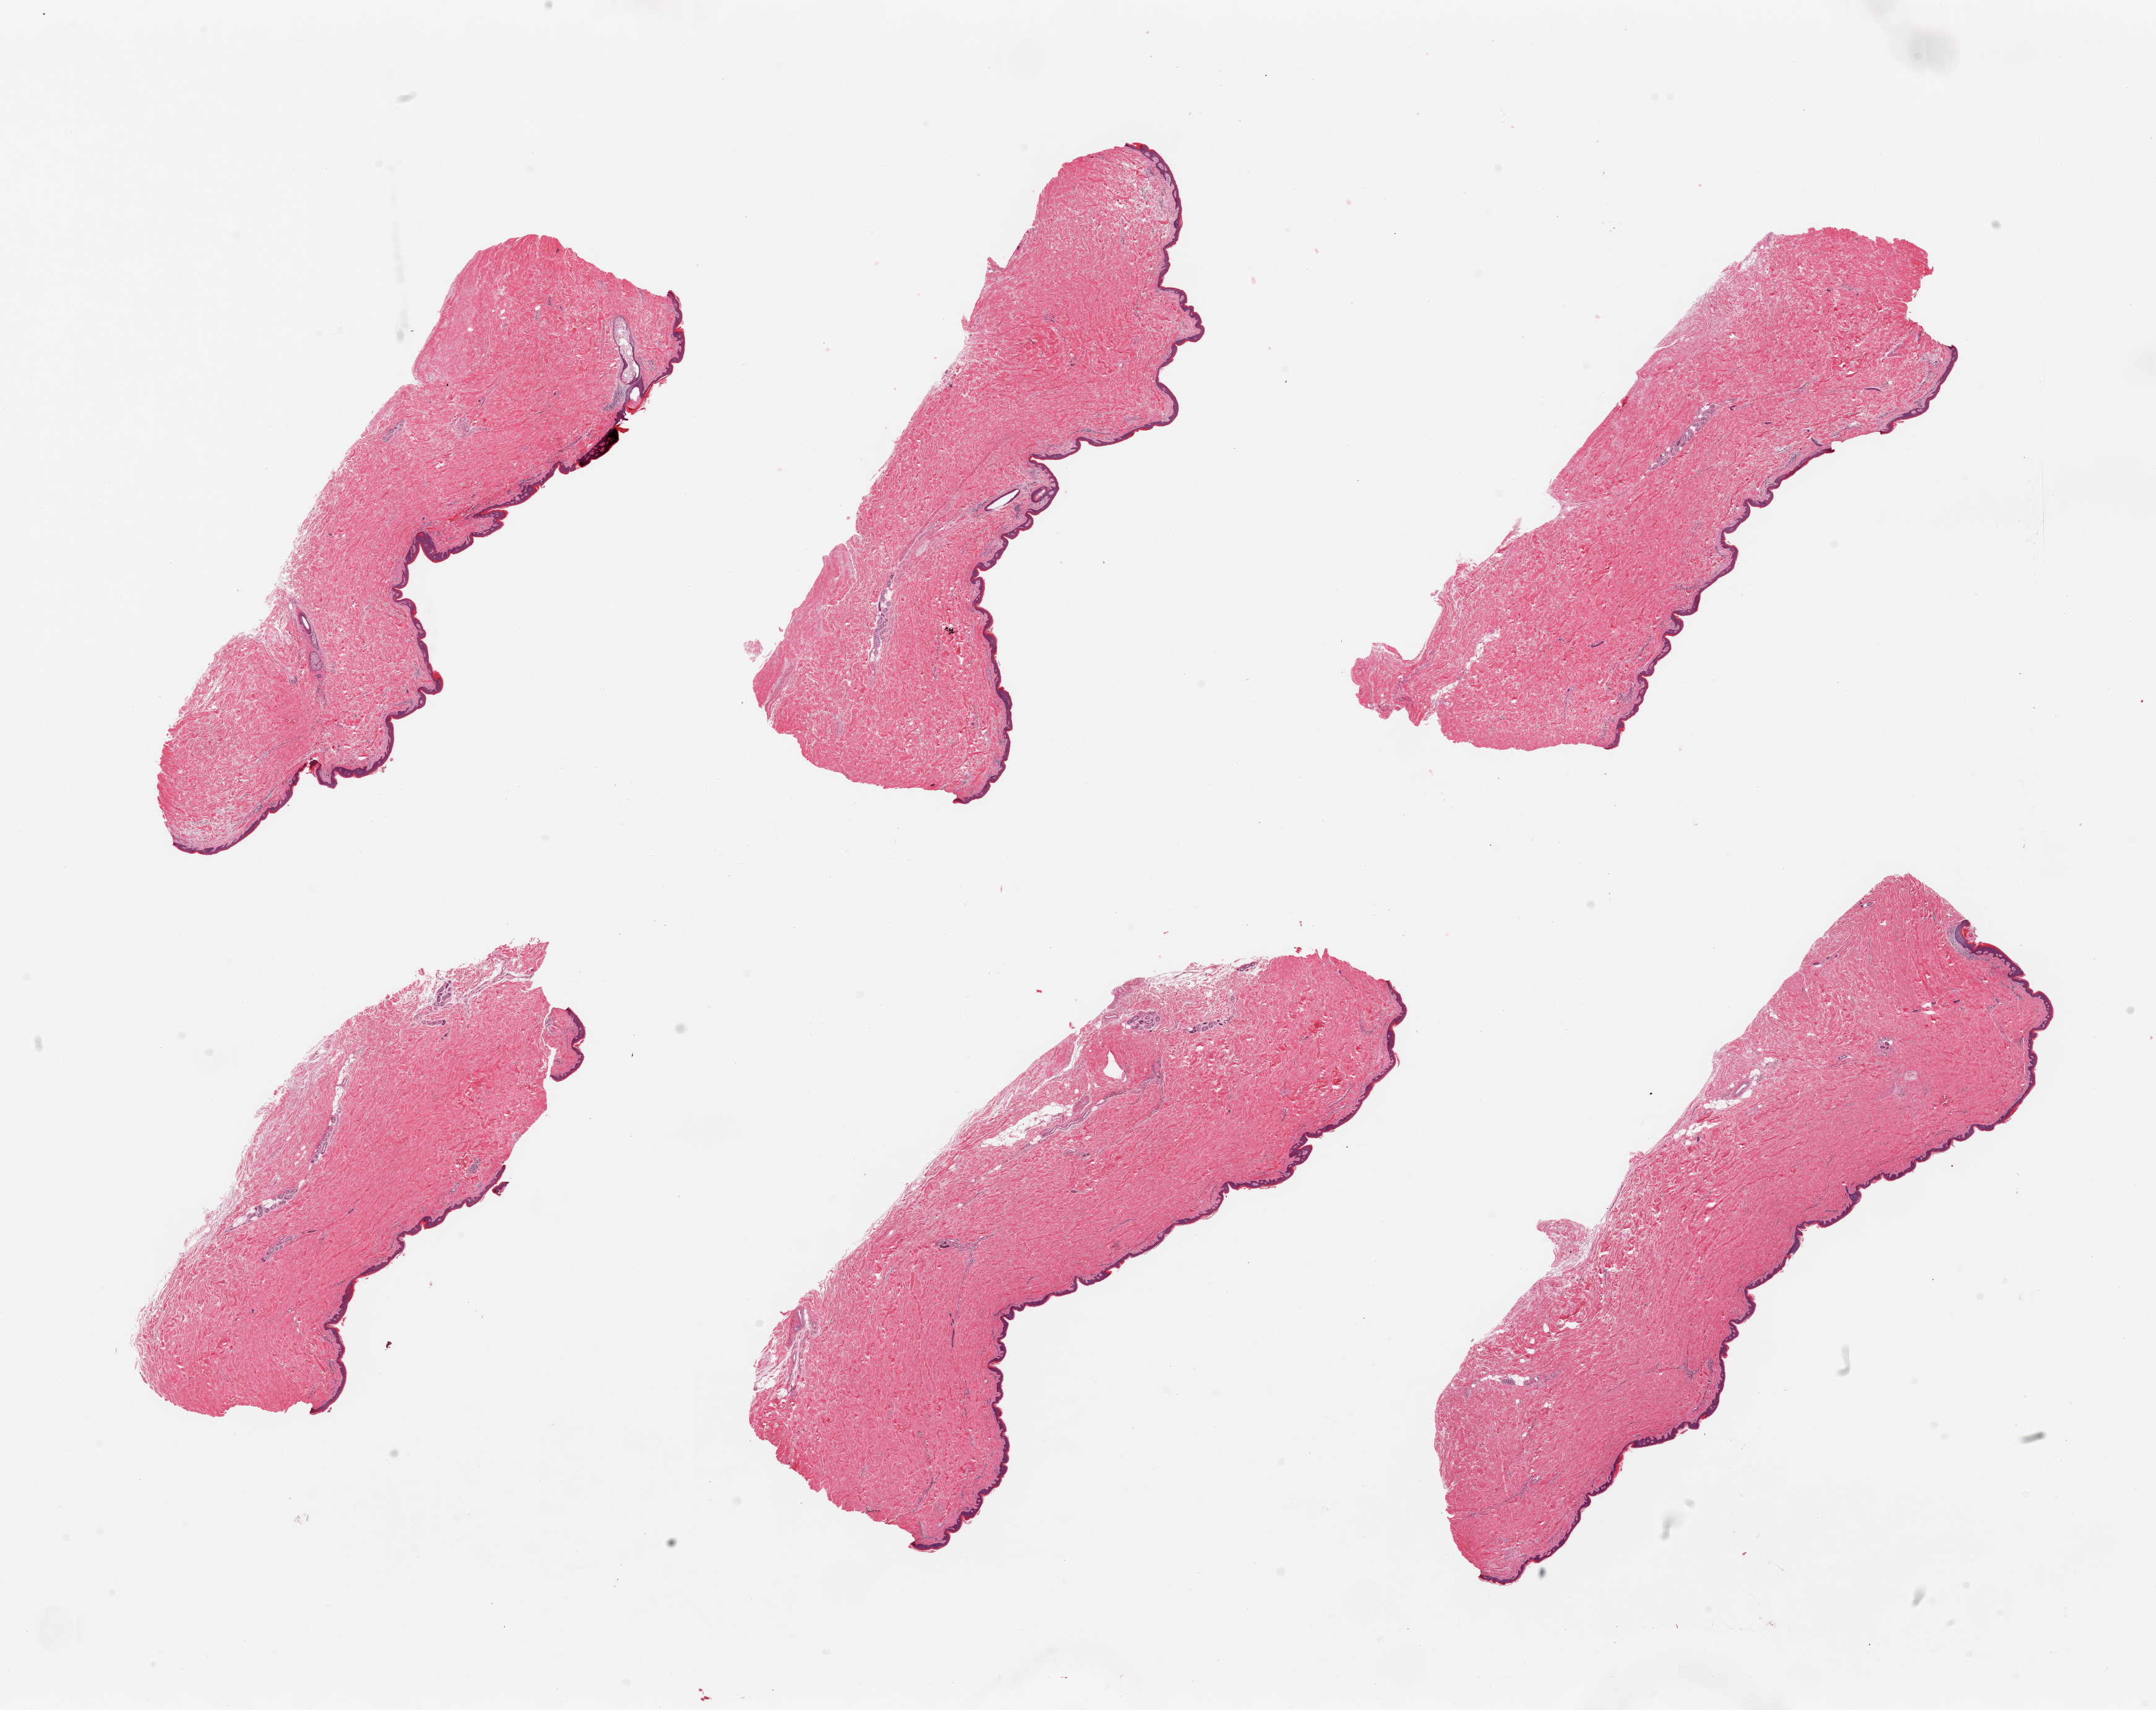
Hematoxylin and eosin (H&E) whole-slide image, brightfield, whole scanned area (about 27.6 x 21.9 mm) shown as a low-resolution overview; PAXgene-fixed paraffin-embedded (PFPE) section; section of skin of suprapubic region (target tissue); tissue donor sample. Donor: male.
• review note (as recorded): 6 pieces, no dermal fat; squamous epithelium is ~50 microns